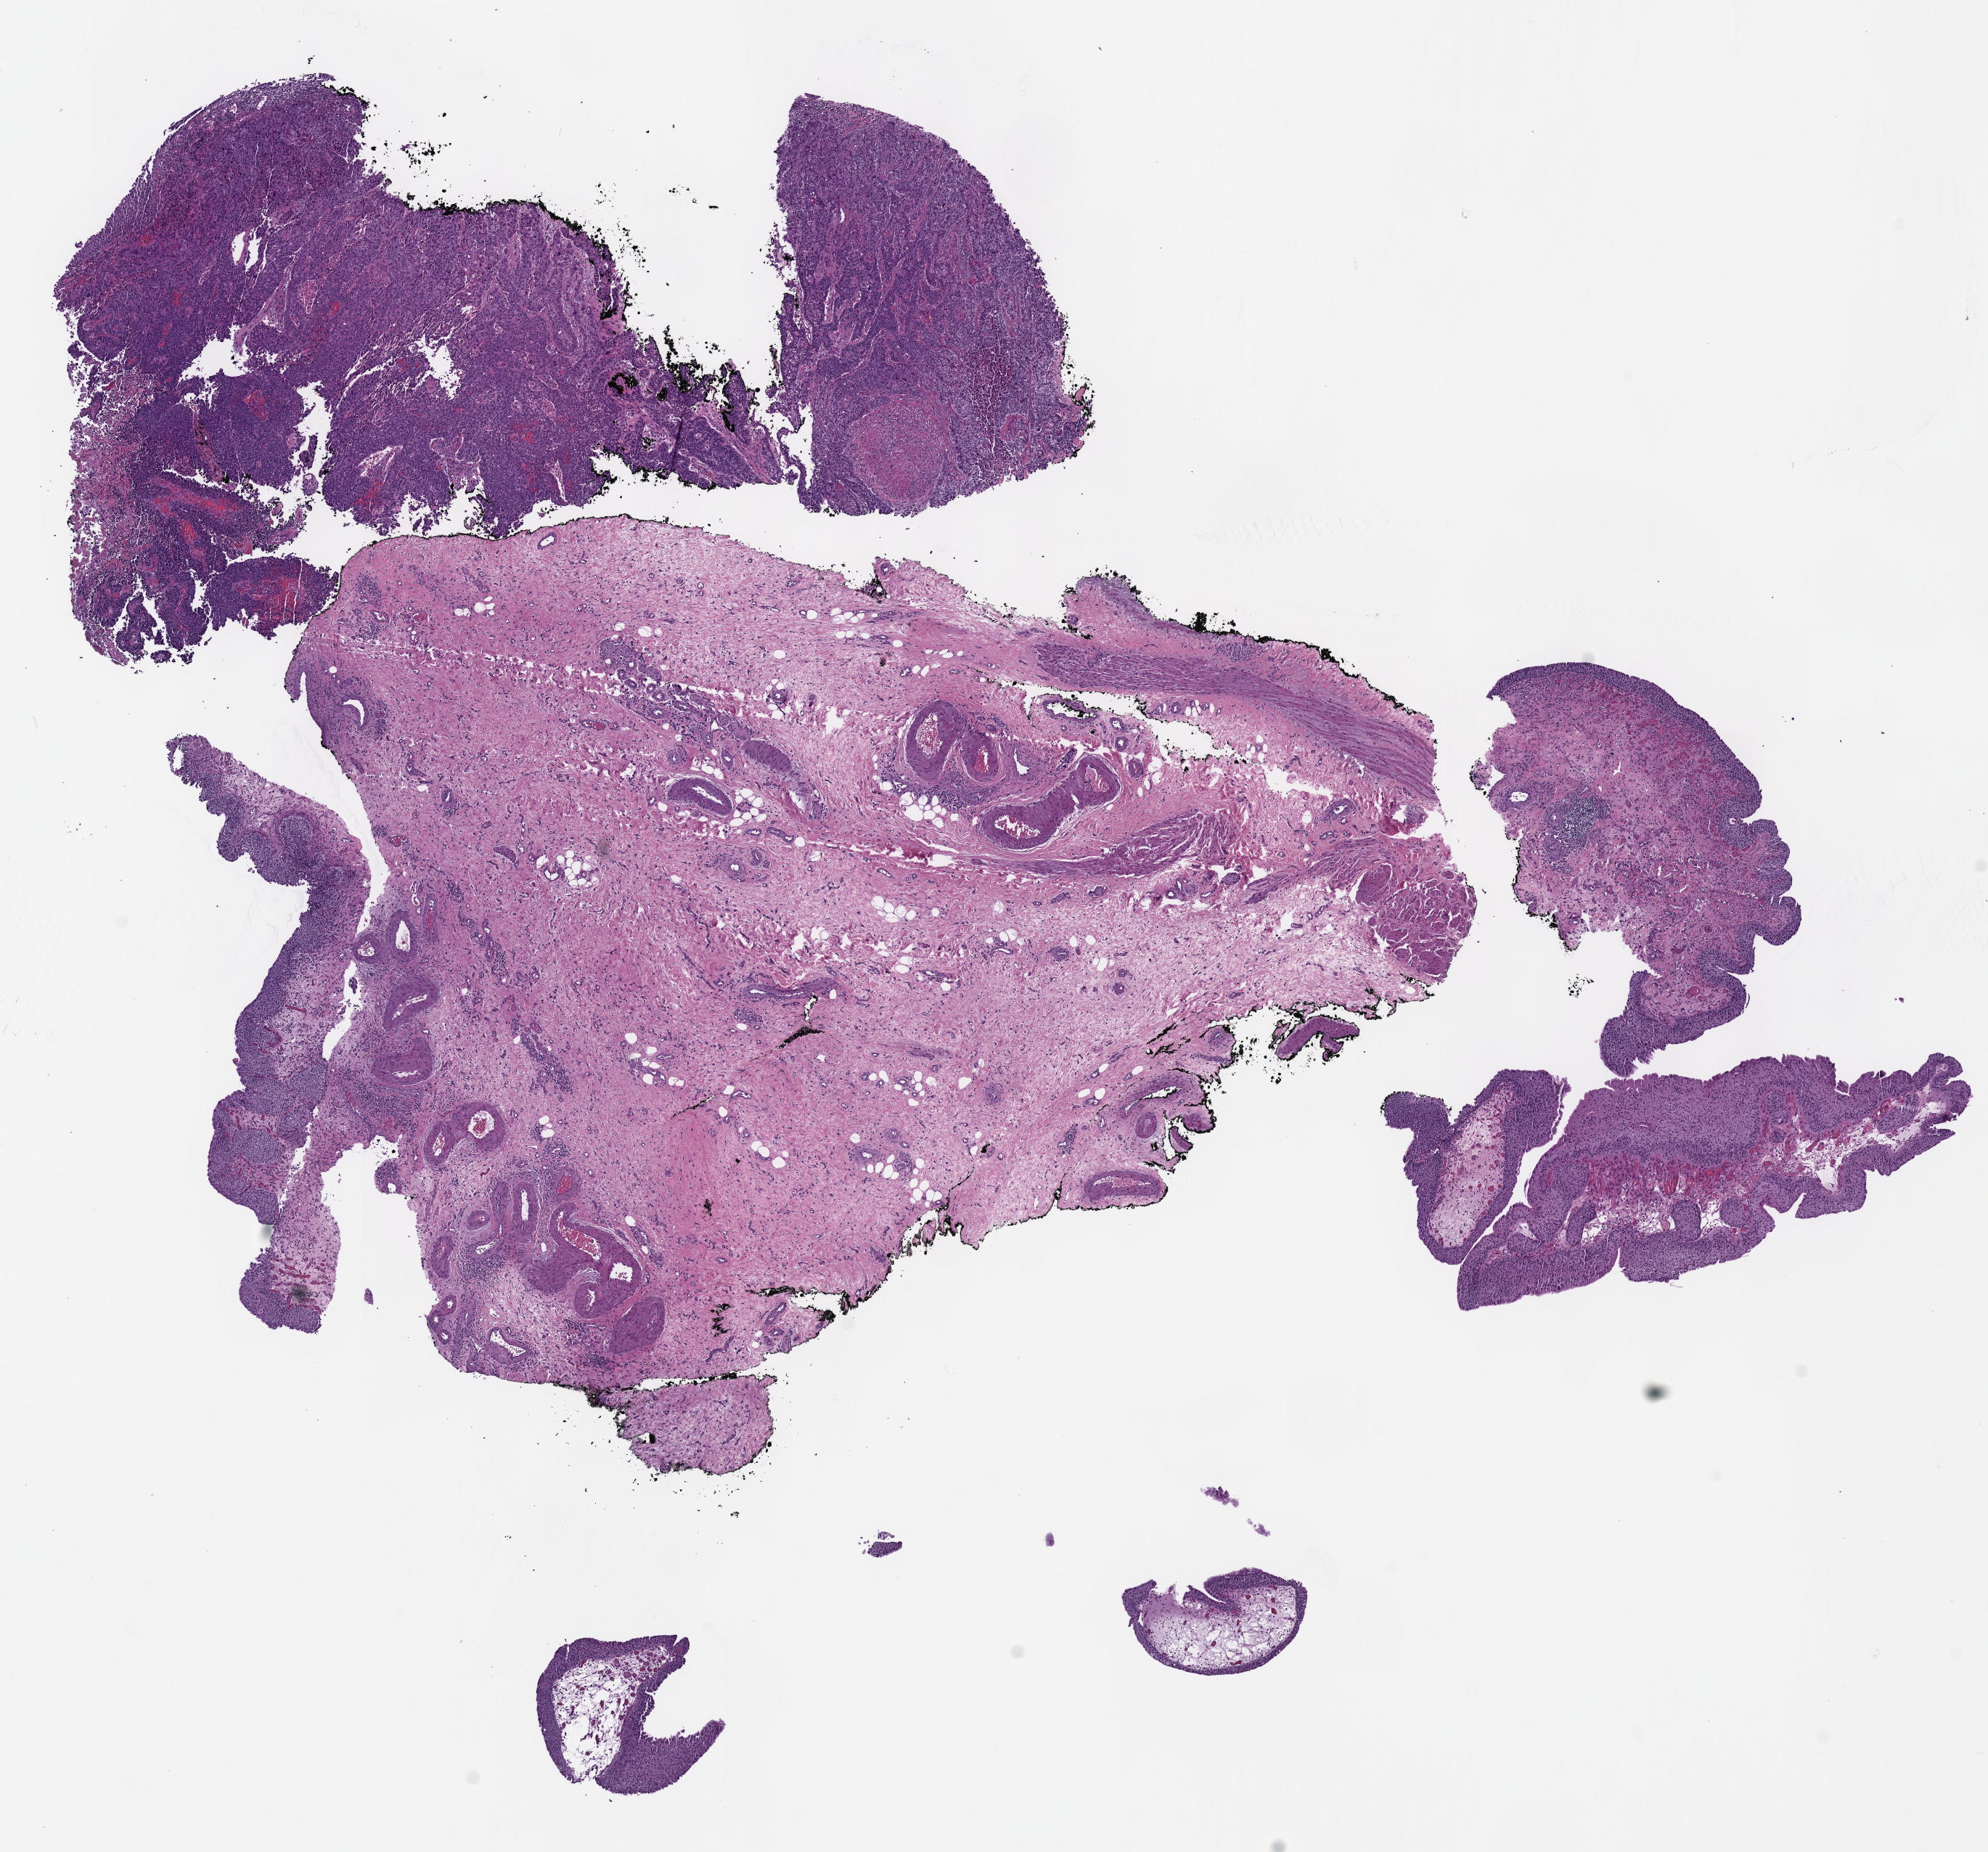
Digitized H&E-stained tissue section (whole slide), shown as a low-resolution overview of the whole scanned area (about 10.8 x 10.0 mm, acquisition: 40x scan), formalin-fixed paraffin-embedded (FFPE) diagnostic section, primary tumour sample from the bladder. Patient: male, age at initial diagnosis 45 years.
Diagnosis: Transitional cell carcinoma.